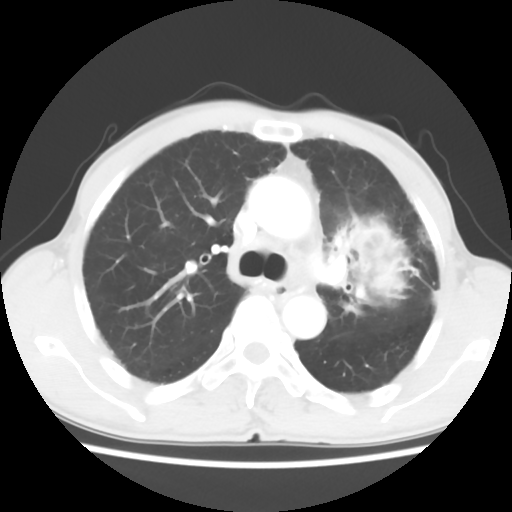
Chest CT, one axial slice. Slice 40 of 60 in the series (ordered by position). Reconstruction kernel STANDARD. Lung window (W 1500 / L -600 HU). 5 mm slice thickness. 512 × 512 image matrix. Patient: male, 64 years. Case-level facts recorded for this patient, not image findings: clinical TNM (as recorded): T3 N3 M0.
Structures marked on this image (rectangle marked by the reading radiologist):
- lung tumour (recorded histology: adenocarcinoma): bounding box (x1, y1, x2, y2) in pixels: (329, 200, 416, 325)